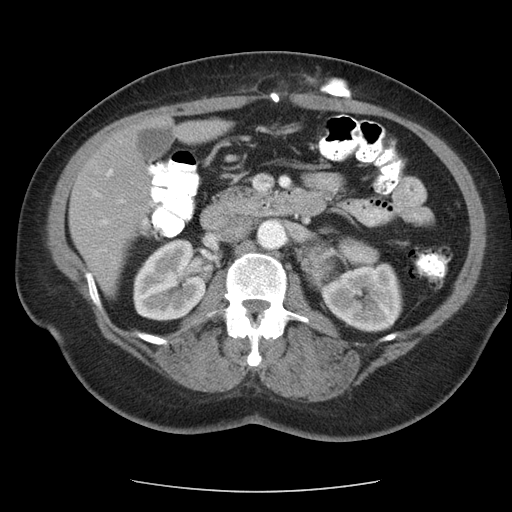
Contrast-enhanced abdominal CT, one axial slice. Position 60 of 95 along the scan axis. Reconstruction kernel STANDARD. Intravenous contrast given. Soft-tissue window (W 400 / L 40 HU). 512 × 512 image matrix, field of view 362 × 362 mm. Patient: female, 71 years. From the clinical record (not read from this slice): diagnosis: adrenocortical carcinoma; tumour side: left adrenal; tumour size at pathology: 8.8 cm; Ki-67 index: 20 %; stage (as recorded): 2.
Structures marked on this image (semi-automatically segmented with operator editing):
- mass: bounding box (x1, y1, x2, y2) in pixels: (305, 246, 333, 281)